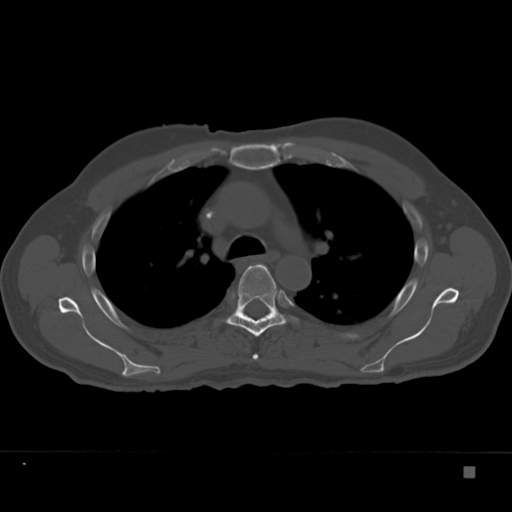
CT including the spine, one axial slice; position 258 of 332 along the scan axis; 120 kVp; bone window (W 1800 / L 400 HU); 1.5 mm slice thickness; 512 × 512 image matrix, field of view 389 × 389 mm. Male patient, age 72 years. Case-level facts recorded for this patient, not image findings: primary cancer: skeletal.
Annotated regions visible in this slice (semi-automatically segmented with operator editing):
- T4 vertebra: bounding box [x1, y1, x2, y2] px = [253, 354, 259, 360]
- T5 vertebra: [226, 264, 297, 337]